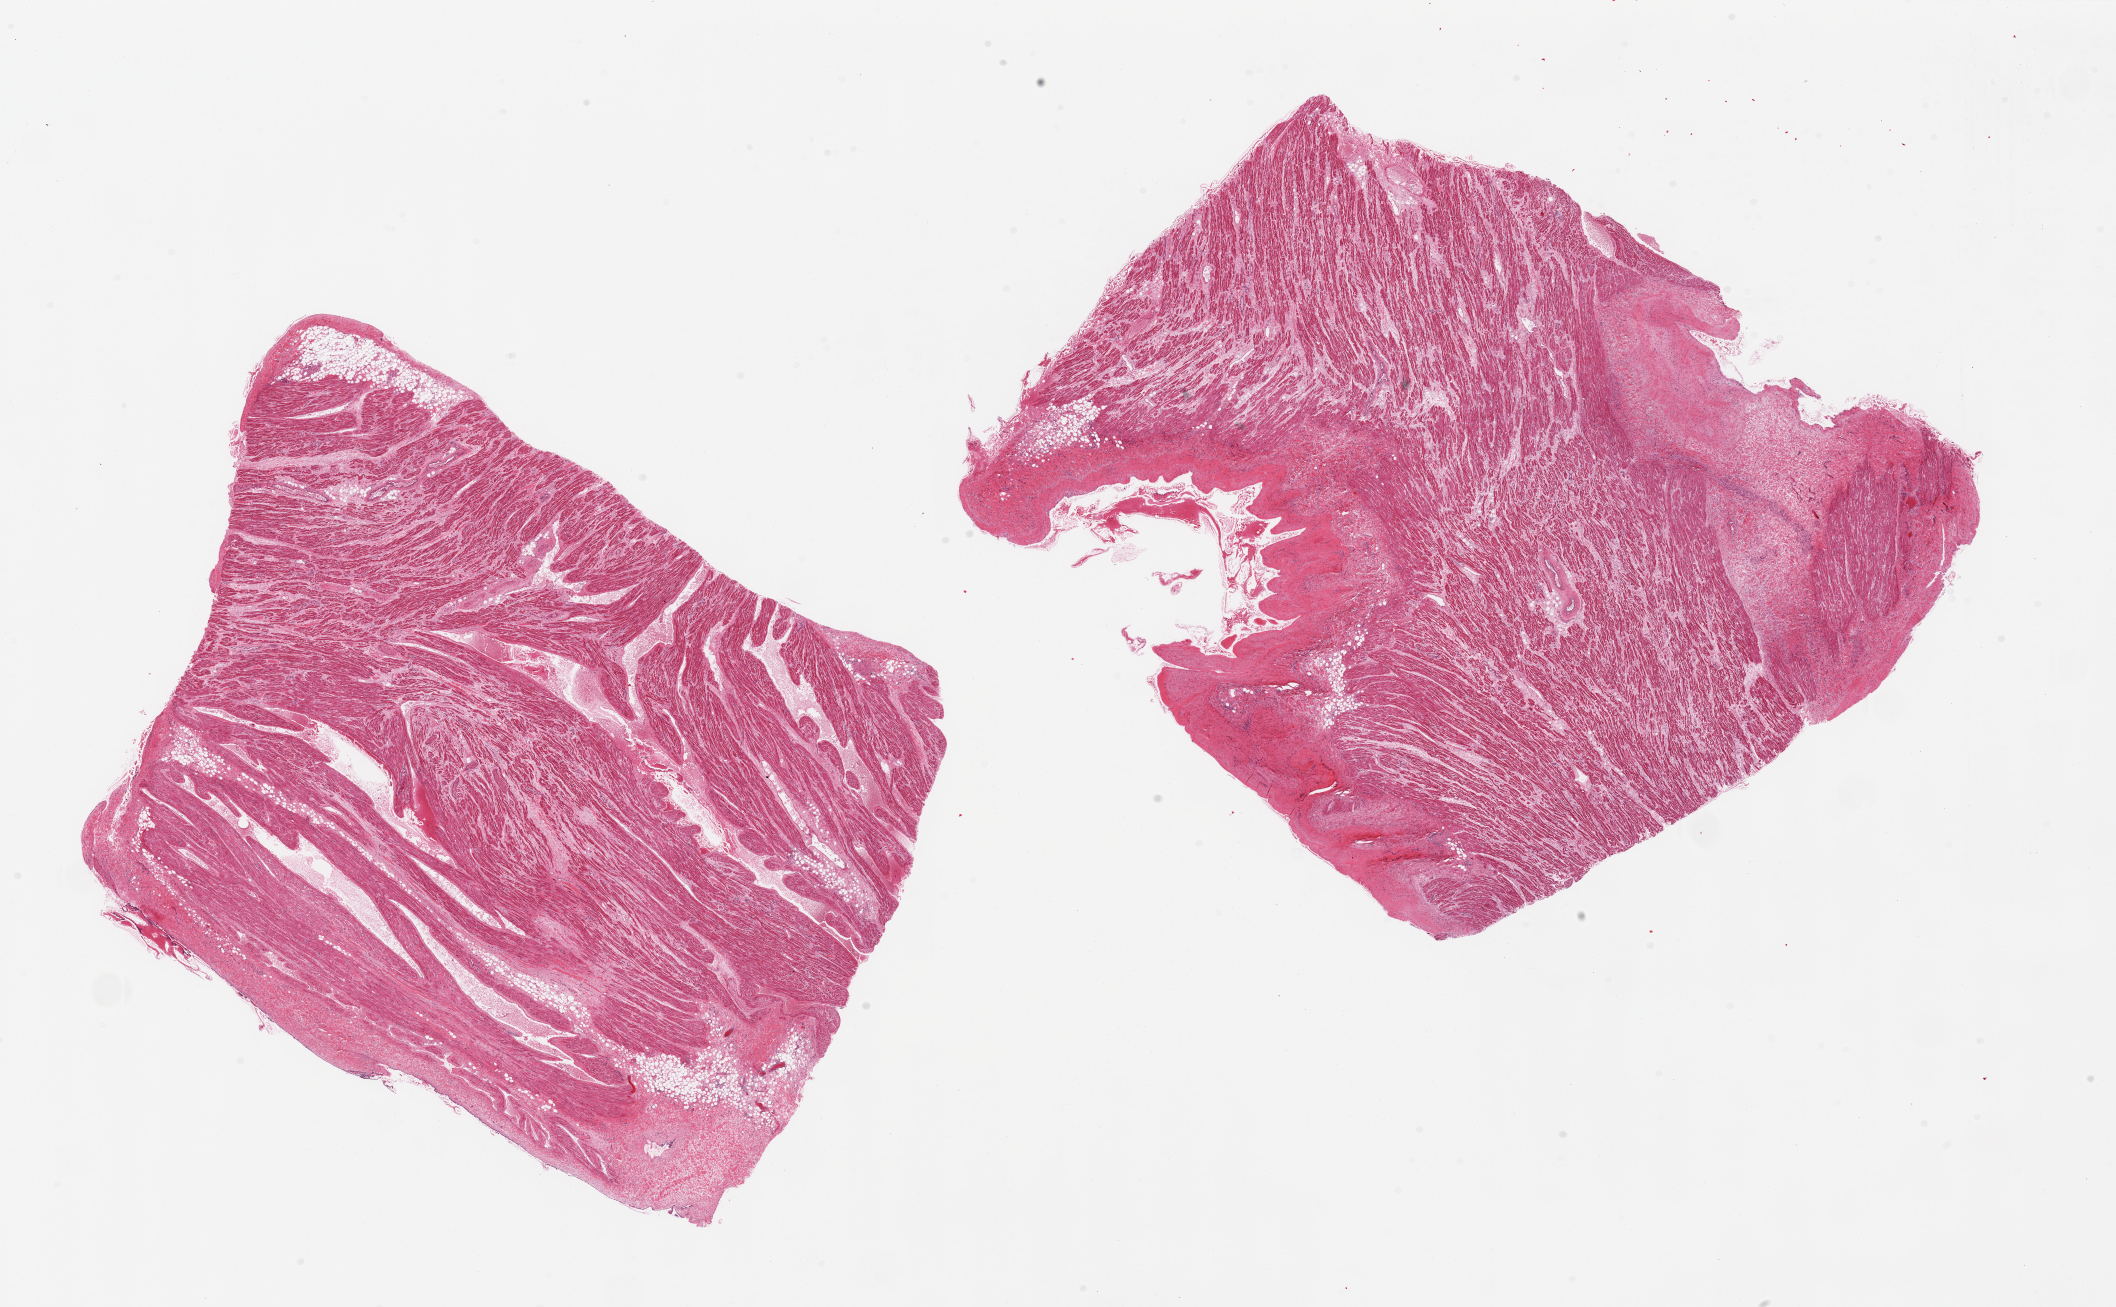
Hematoxylin and eosin (H&E) whole-slide image, whole scanned area (about 33.5 x 20.7 mm) shown as a low-resolution overview. PAXgene-fixed paraffin-embedded (PFPE) section. Section of auricular appendage (target tissue). Donor tissue sample. Donor sex: male.
Reviewer comment on this tissue sample: 2 pieces; 1 piece has 30% fibrous component.